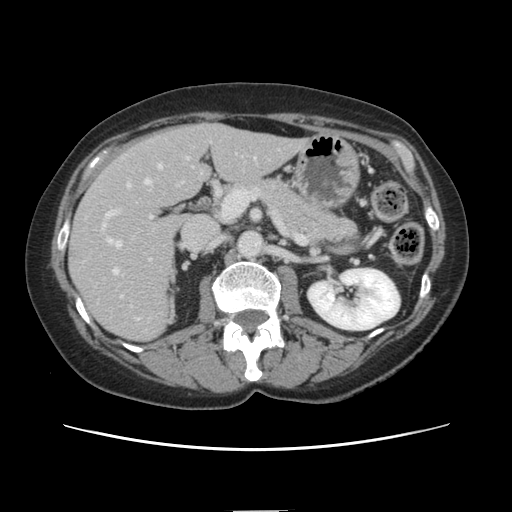
Contrast-enhanced abdominal CT, one axial slice. Slice 66 of 141 in the series (ordered by position). 120 kVp. Intravenous contrast given. Soft-tissue window (W 400 / L 40 HU). 2.5 mm slice thickness. 512 × 512 image matrix, field of view 350 × 350 mm. Female patient, age 63 years. Case-level facts recorded for this patient, not image findings: diagnosis: colorectal cancer liver metastases, imaged before liver resection; multiple liver metastases: yes; largest metastasis: 3.2 cm; chemotherapy before resection: yes.
Structures marked on this image (outlined manually by an expert reader):
- hepatic veins: box from (x=109, y=165) to (x=161, y=276) px
- liver: (x=70, y=125)–(x=304, y=340)
- planned liver remnant (the part of the liver to remain after resection): (x=176, y=125)–(x=305, y=190)
- portal vein (with intrahepatic branches): (x=103, y=182)–(x=132, y=227)
- liver metastasis: (x=69, y=249)–(x=76, y=257)